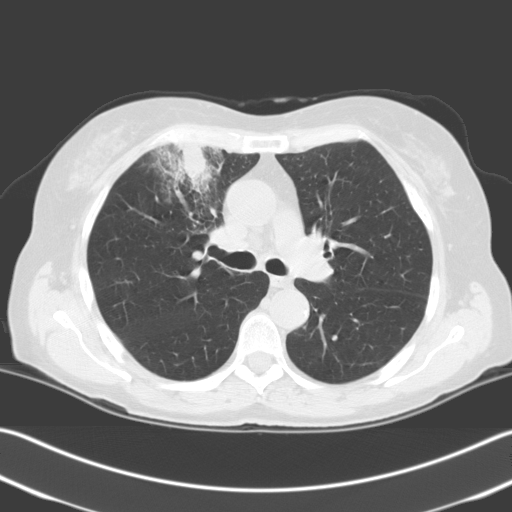
Low-dose screening chest CT, one axial slice. Slice 138 of 204 in the series (ordered by position). 140 kVp. Lung window (W 1500 / L -600 HU). 3.2 mm slice thickness. 512 × 512 image matrix, field of view 348 × 348 mm.
Annotated regions visible in this slice (expert manual segmentation):
- lesion 1 (tumor, upper lobe of right lung): bounding box (x1, y1, x2, y2) in pixels: (174, 142, 213, 191)